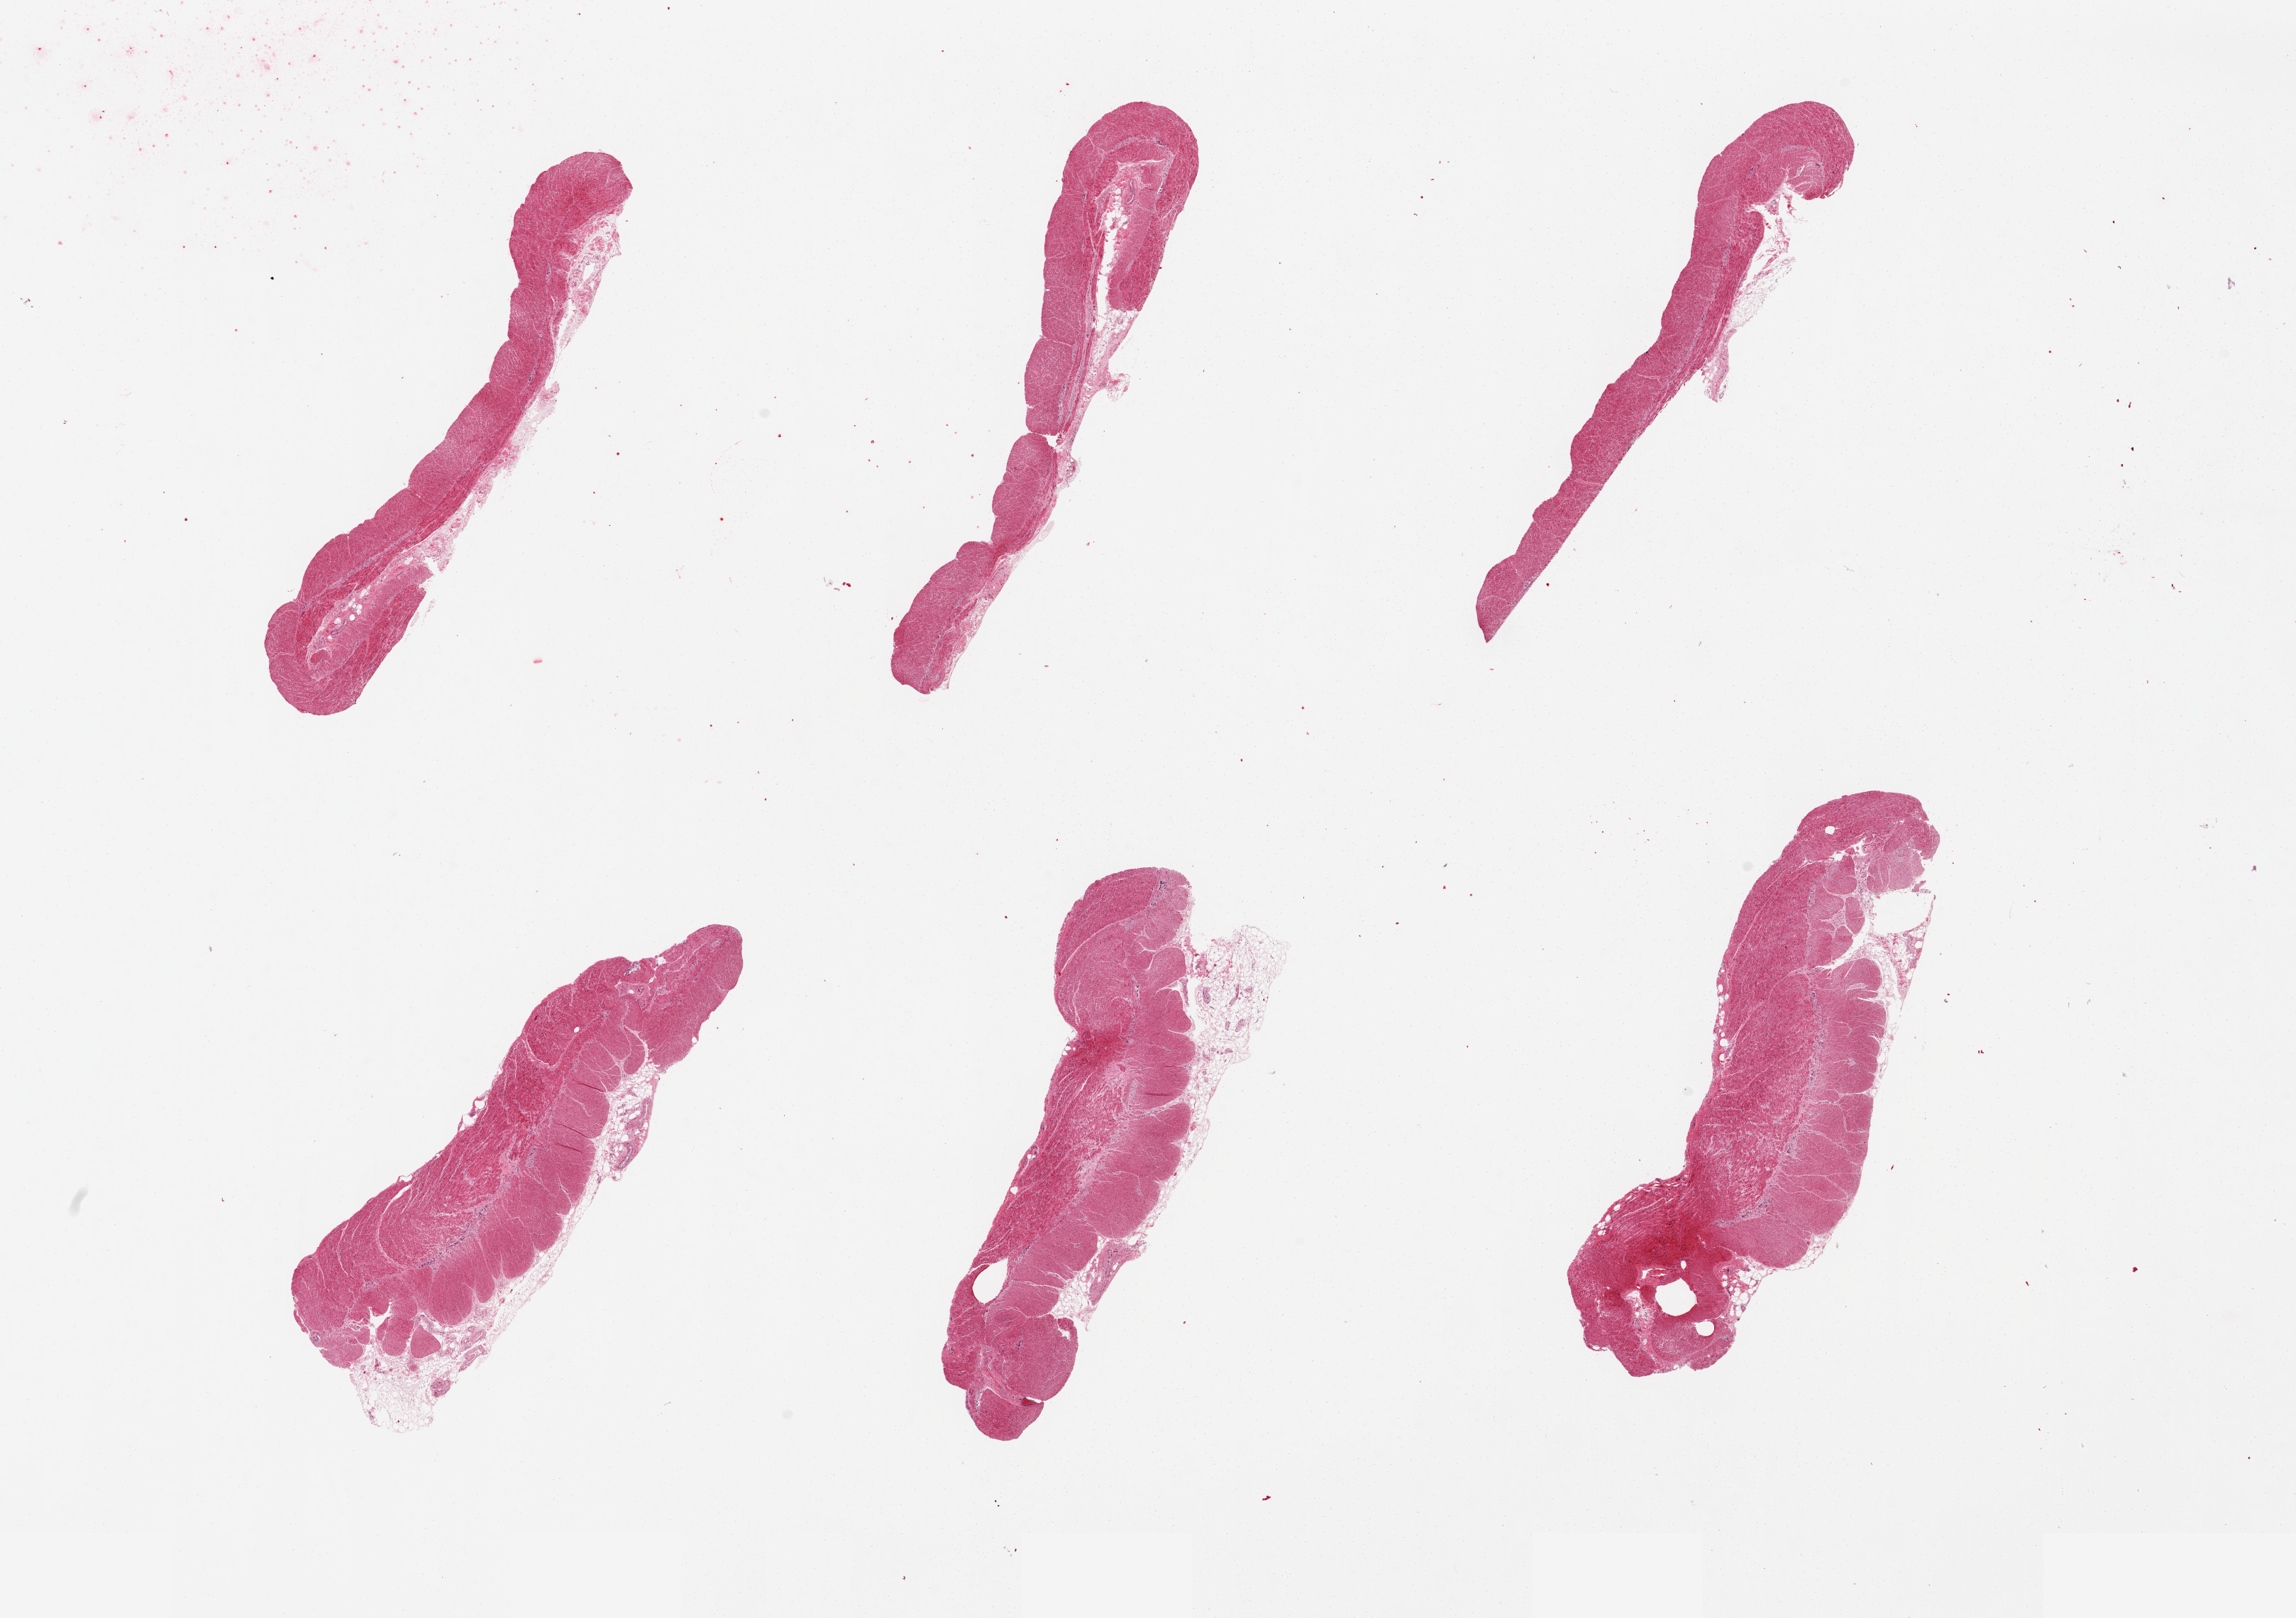
Whole-slide image, H&E stain, low-resolution overview of the scanned area, about 25.6 x 18.0 mm. PAXgene-fixed, paraffin-embedded tissue. Target tissue: sigmoid colon. Tissue donor sample. Female donor.
Review note (as recorded): 6 pieces, all muscularis, good specimens.